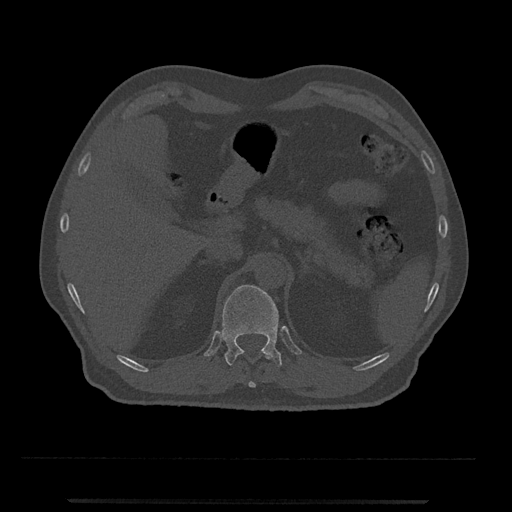
CT including the spine, one axial slice; slice 420 of 797 in the series (ordered by position); 120 kVp; bone window (W 1800 / L 400 HU); 512 × 512 image matrix, field of view 419 × 419 mm. Patient: male, 63 years. From the clinical record (not read from this slice): primary cancer: prostate.
Structures marked on this image (semi-automatic segmentation, software-assisted and operator-edited):
- T11 vertebra: bounding box [x1, y1, x2, y2] px = [236, 350, 272, 388]
- T12 vertebra: [222, 285, 282, 367]